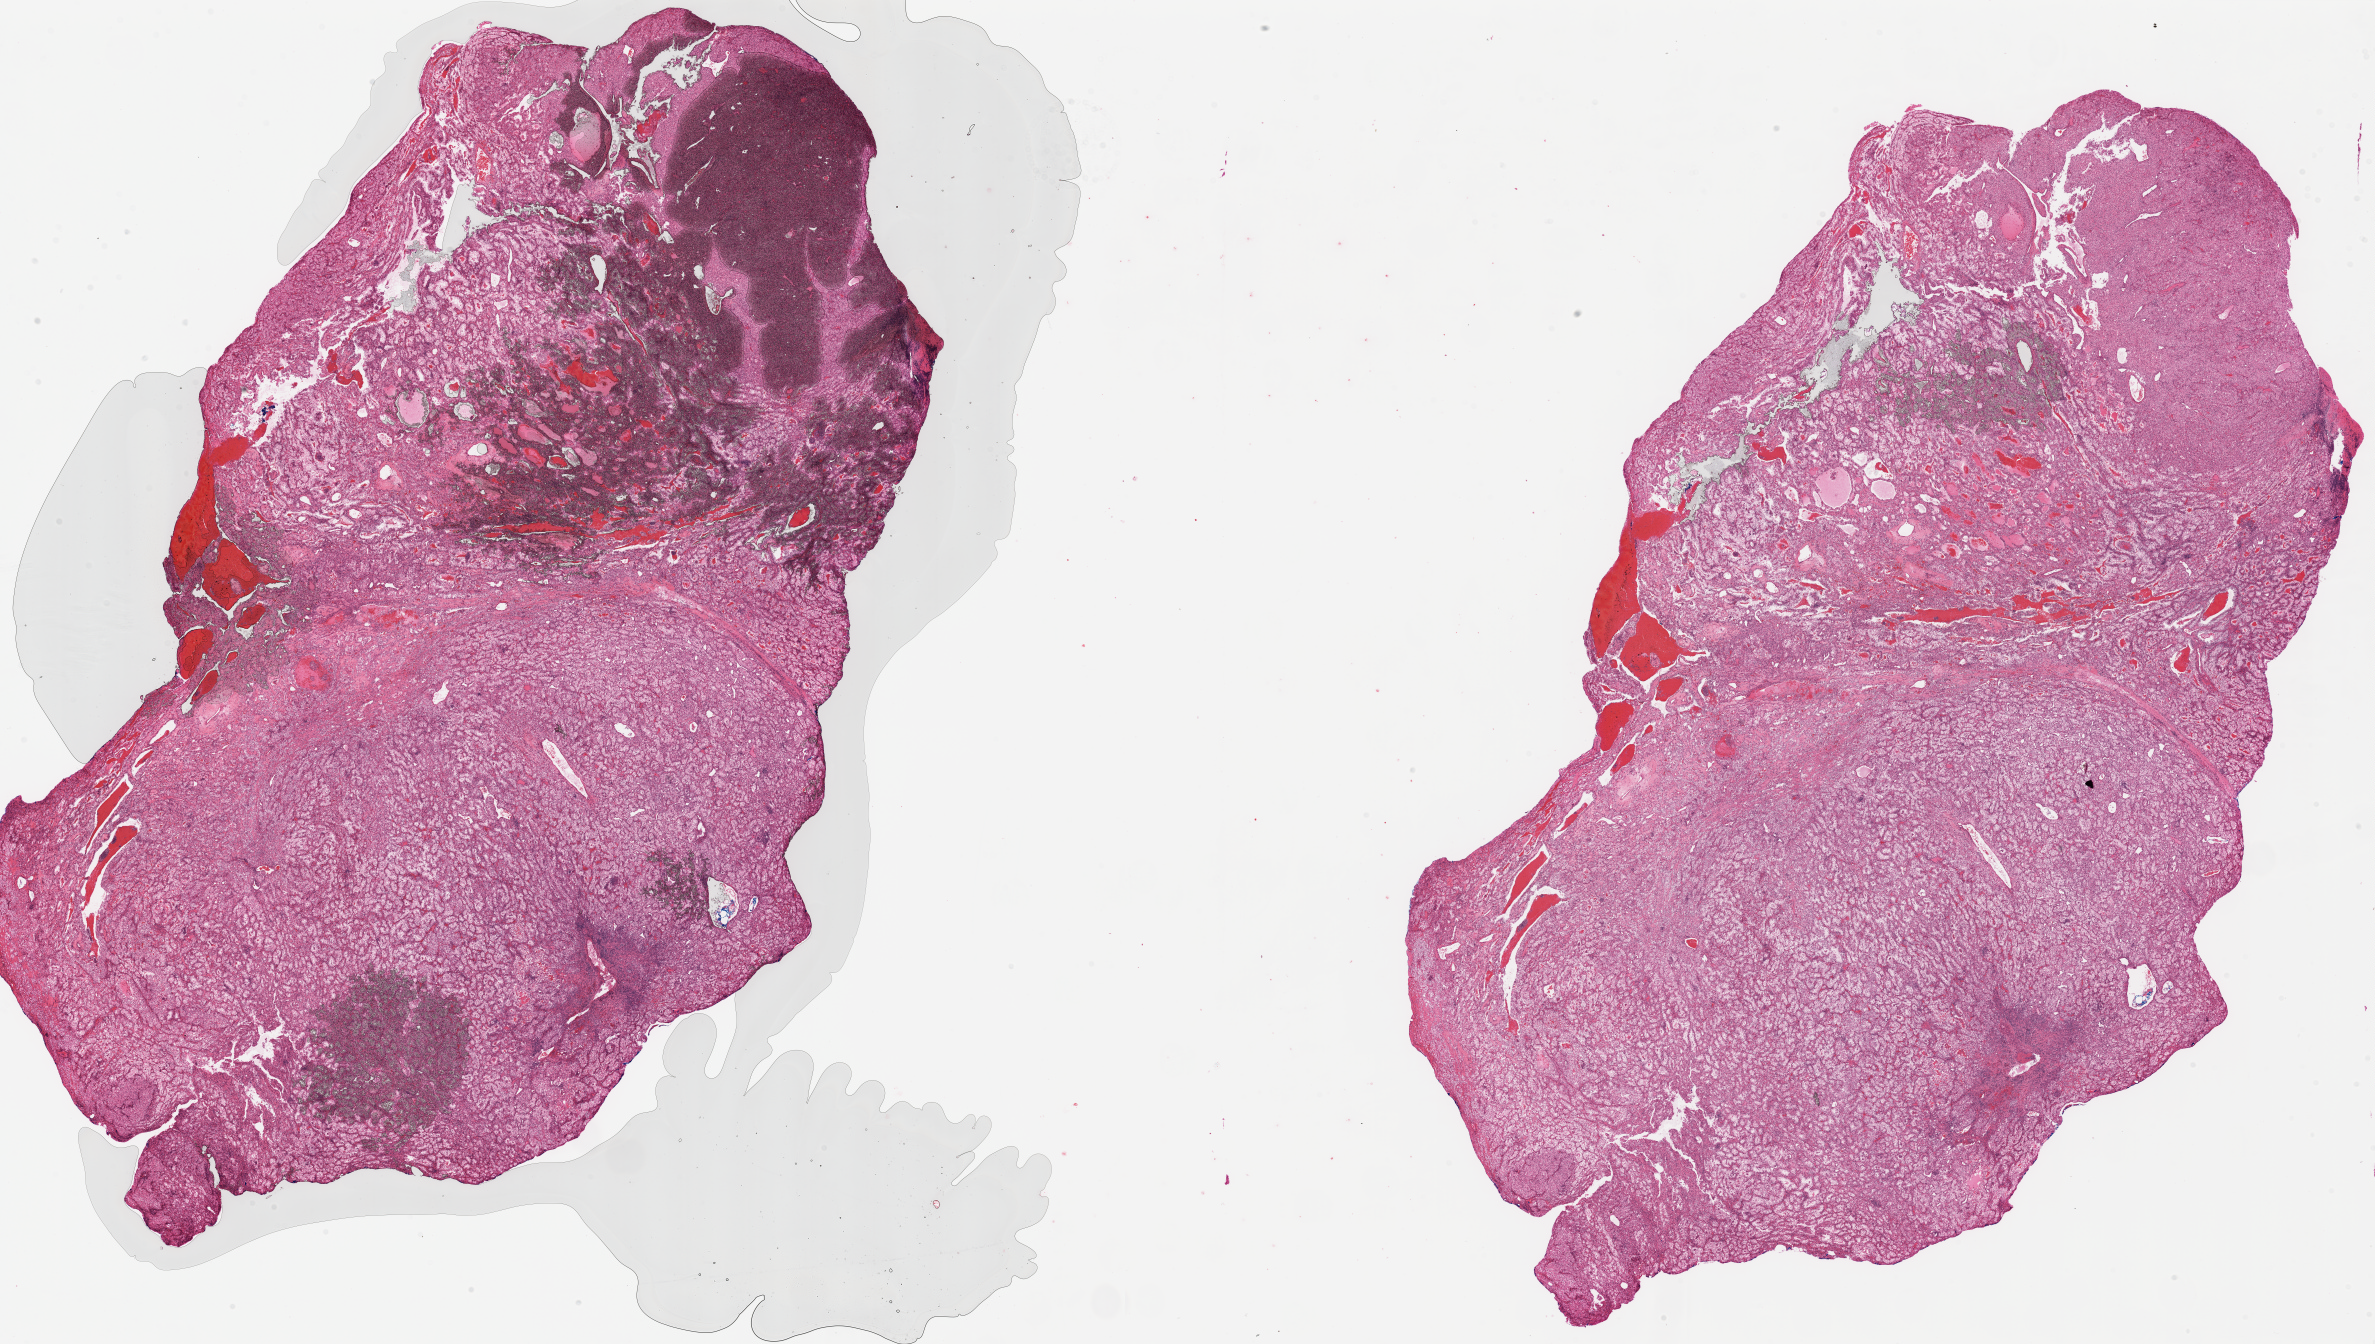
Whole-slide histology image, H&E-stained — a low-resolution overview of the entire scanned area, about 37.6 x 21.3 mm; formalin-fixed paraffin-embedded (FFPE) diagnostic section; sample: primary tumour, kidney. Female, age 63 years at initial diagnosis. Histologic grade: G3 (poorly differentiated).
Laterality: right. Histologic diagnosis: Clear cell adenocarcinoma, NOS. AJCC pathologic stage: III.